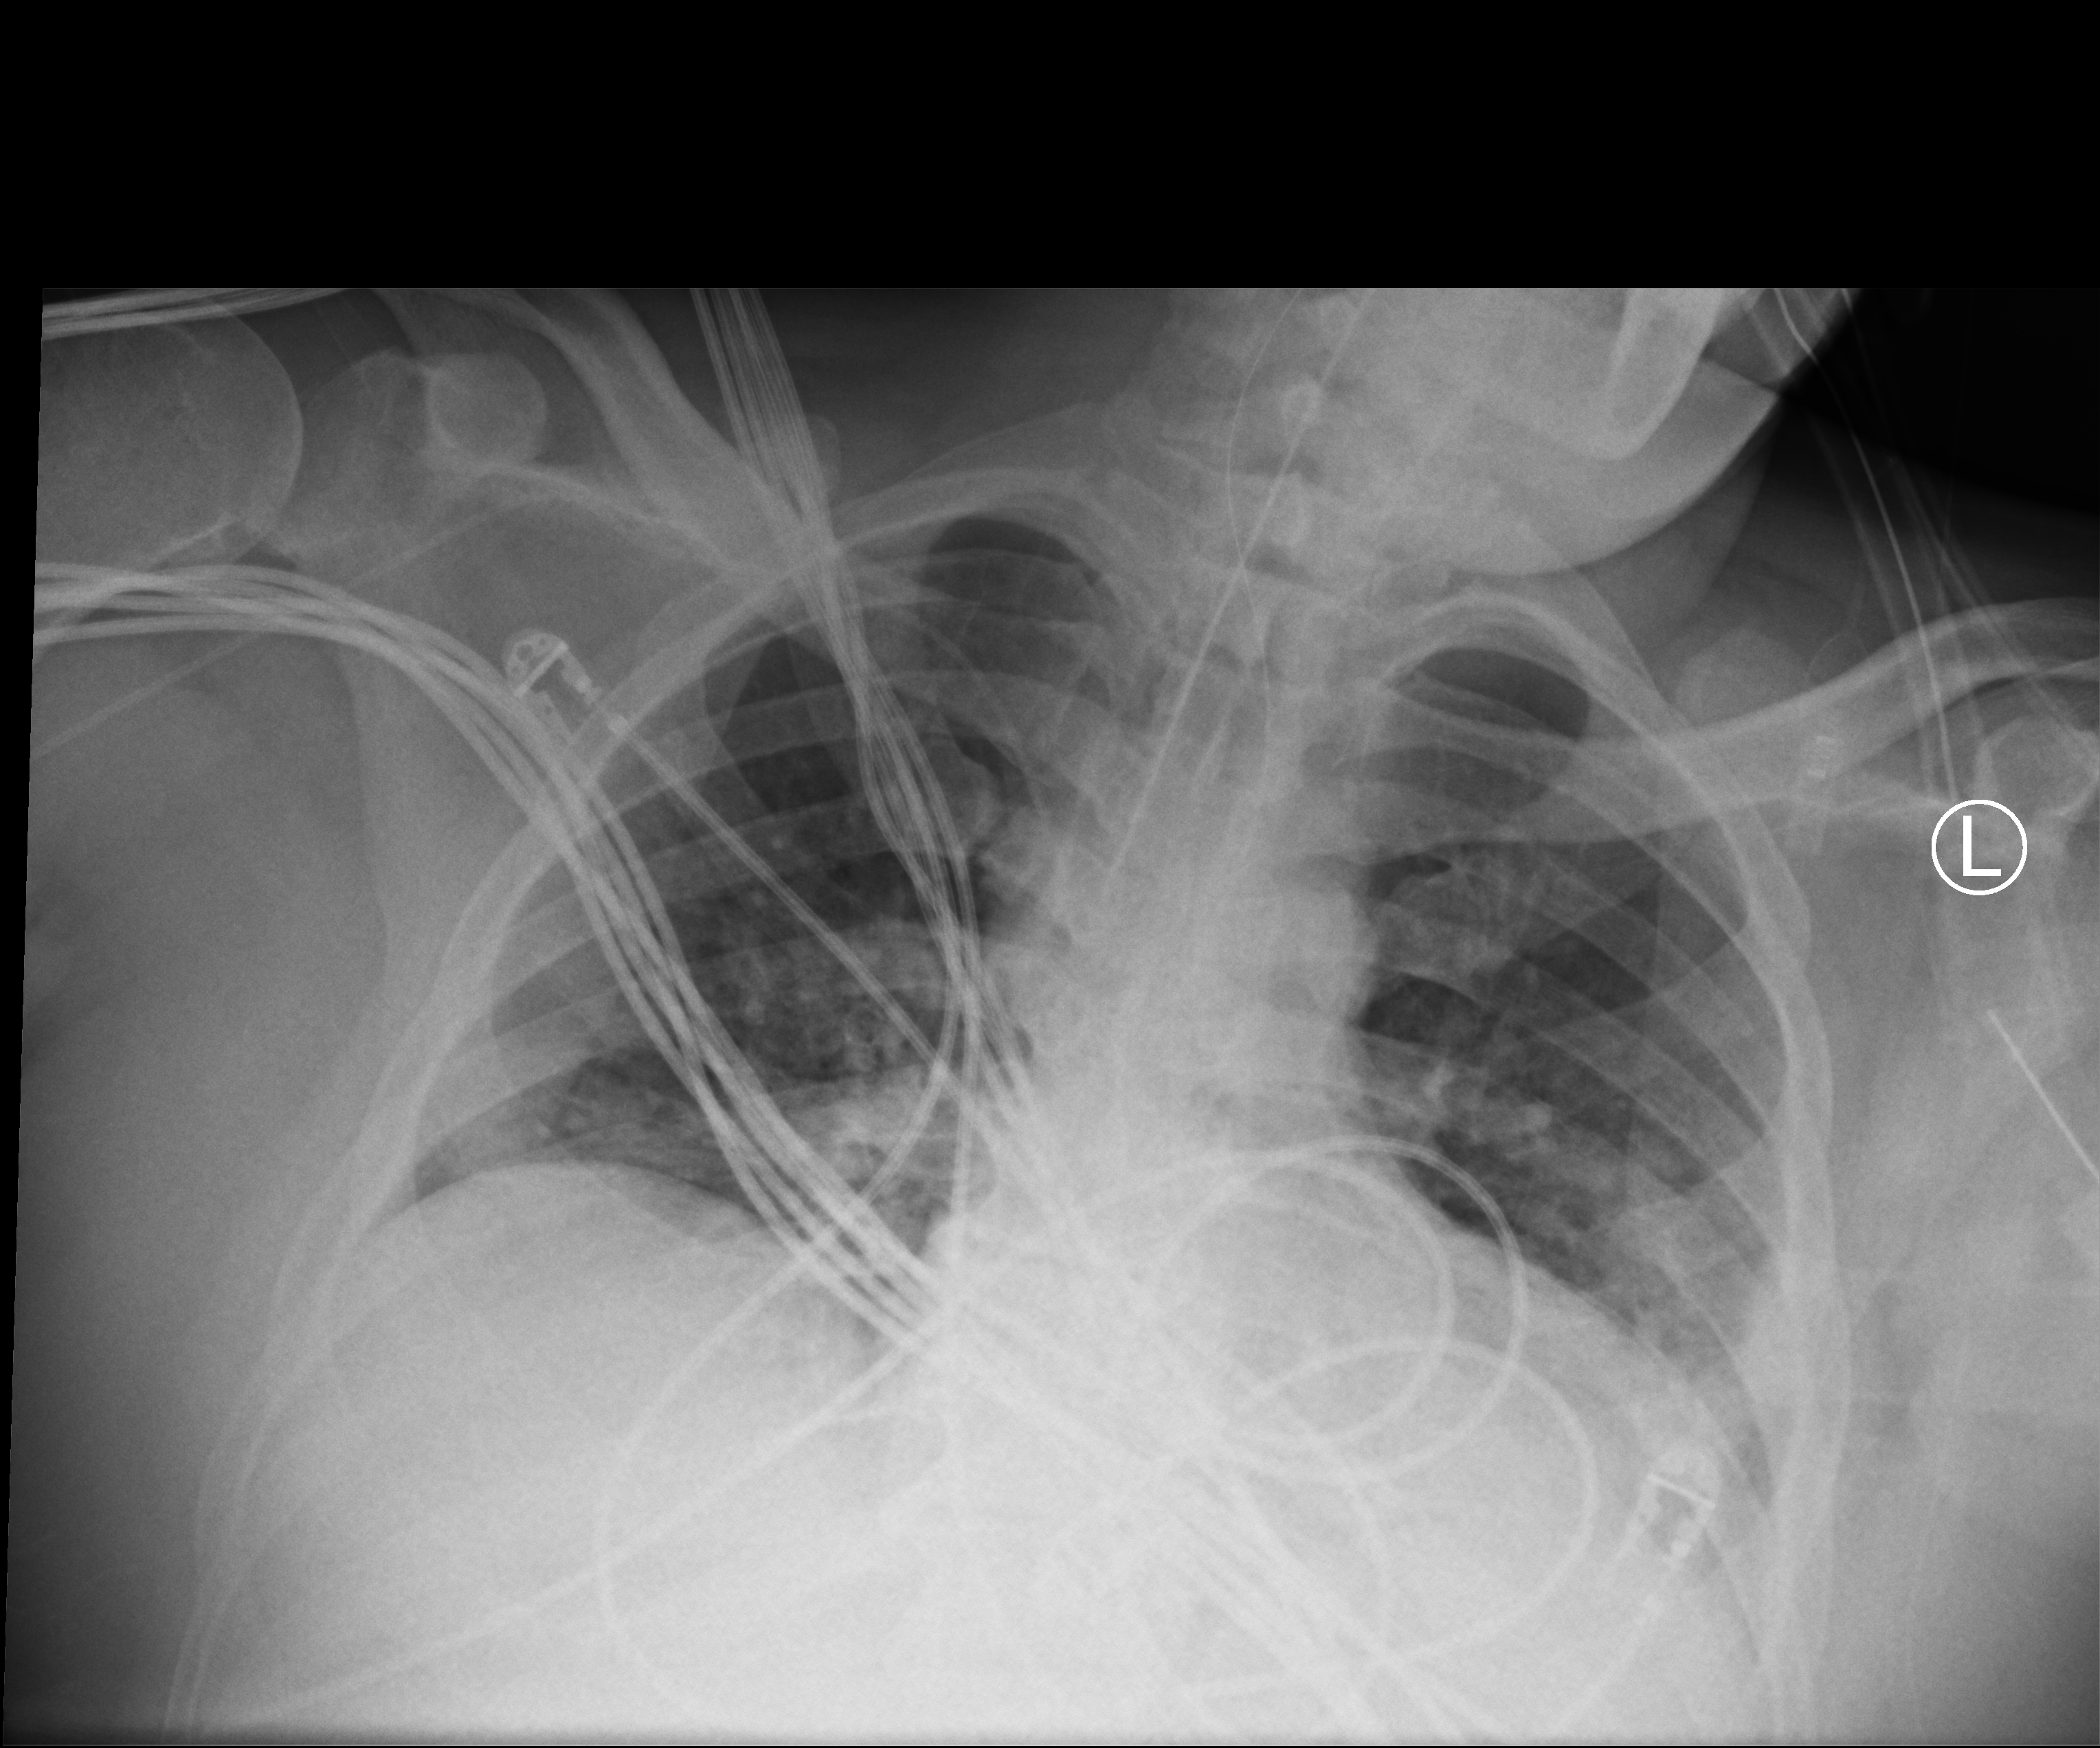
Bedside chest radiograph (computed radiography); anteroposterior (AP) projection. Male patient hospitalised with COVID-19, age 18–59 years.
Hospital-stay facts (about this admission, not read from this image; timing relative to this image not recorded): admitted to intensive care during this hospital stay: yes; hypertension (admission record): no; mechanically ventilated during this hospital stay: yes.